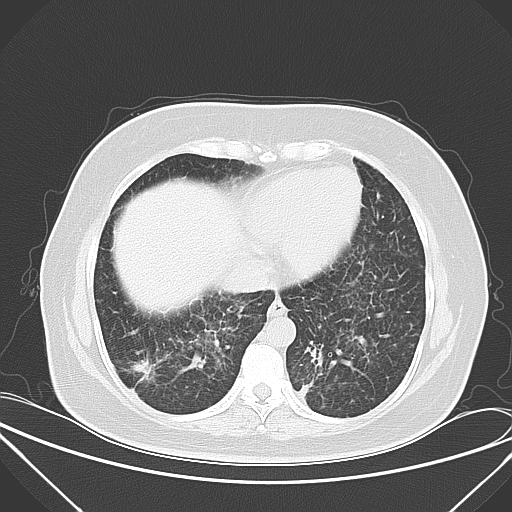
Chest CT, one axial slice. Position 15 of 52 along the scan axis. 120 kVp. Lung window (W 1500 / L -600 HU). 5 mm slice thickness. 512 × 512 image matrix, field of view 386 × 386 mm. Female patient, age 50 years. From the clinical record (not read from this slice): clinical TNM (as recorded): T1c N0 M1a.
Annotated regions visible in this slice (bounding box drawn by a radiologist):
- lung tumour (recorded histology: adenocarcinoma): box from (x=126, y=352) to (x=161, y=390) px